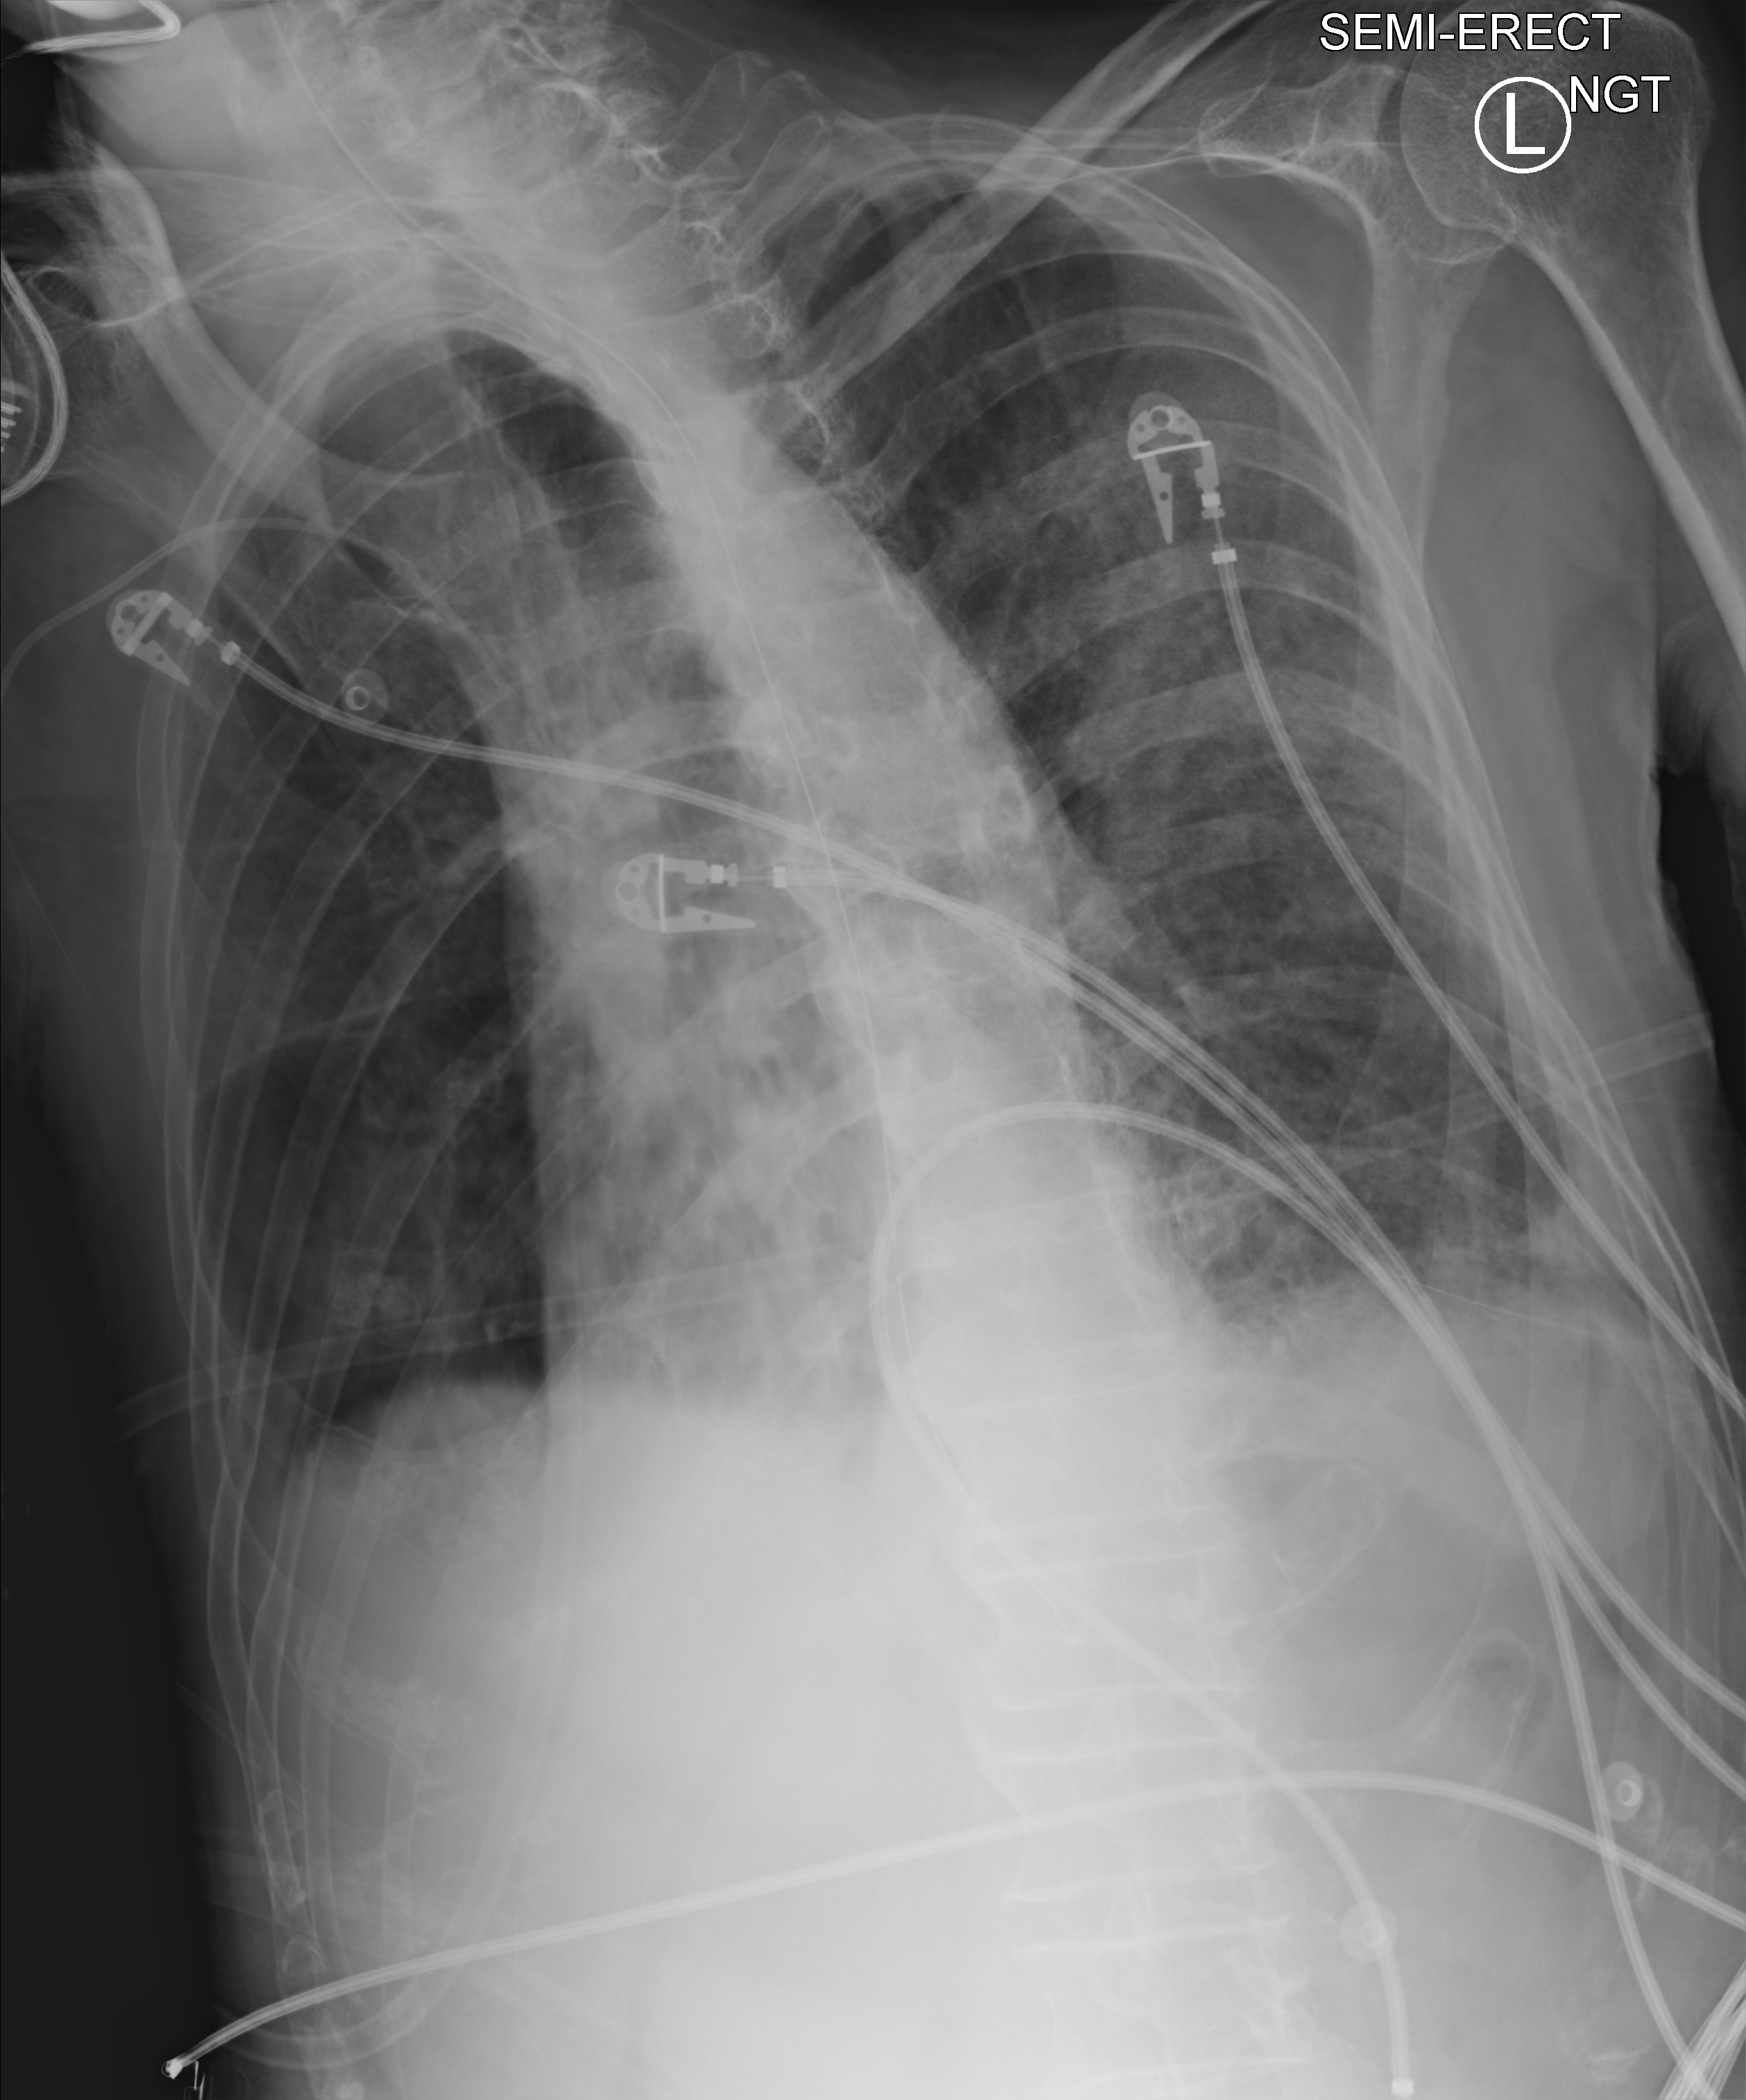
Portable chest radiograph. Patient hospitalised with COVID-19; male, aged 60–74 years.
Admission-level facts for this patient (not findings on this image; timing relative to this image not recorded): smoking status (admission record): current; diabetes (admission record): yes; admitted to intensive care during this hospital stay: yes.